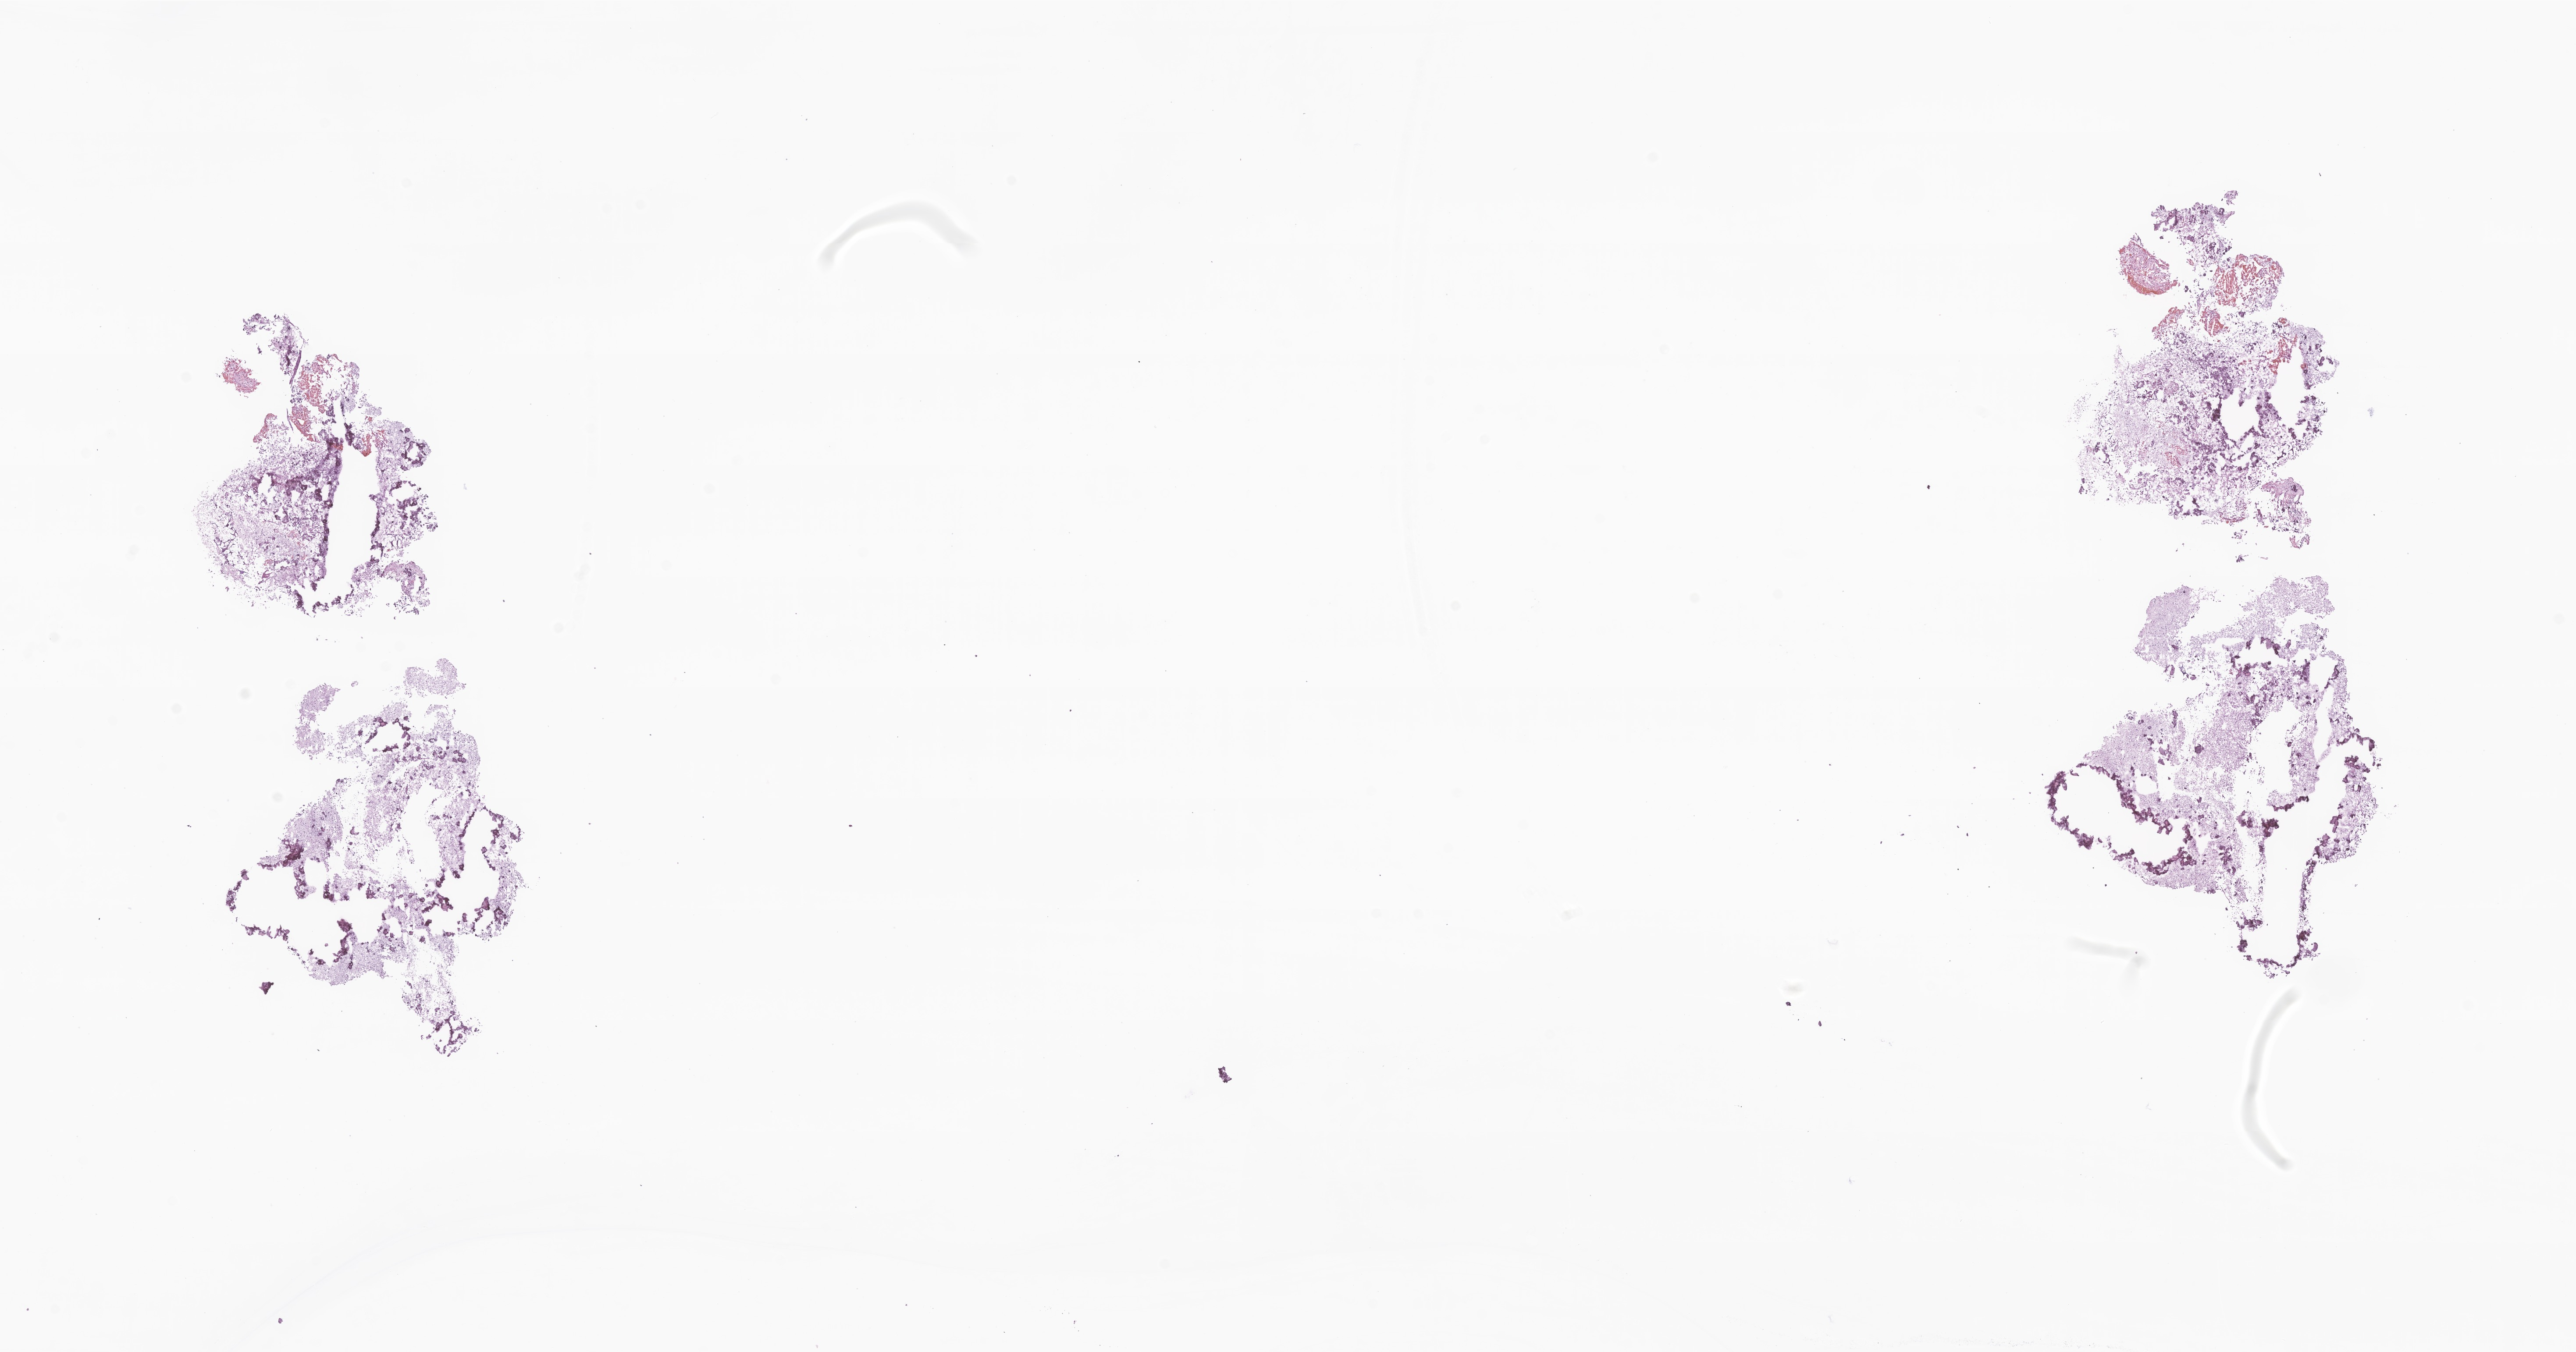
Hematoxylin and eosin (H&E) whole-slide image of tumor tissue from the brain, low-resolution overview of the scanned area, about 24.8 x 13.0 mm, frozen section (OCT-embedded). Patient: female, age 118 months (9 years 10 months).
Diagnosis (ICD-O-3 morphology term): Neoplasm, benign.